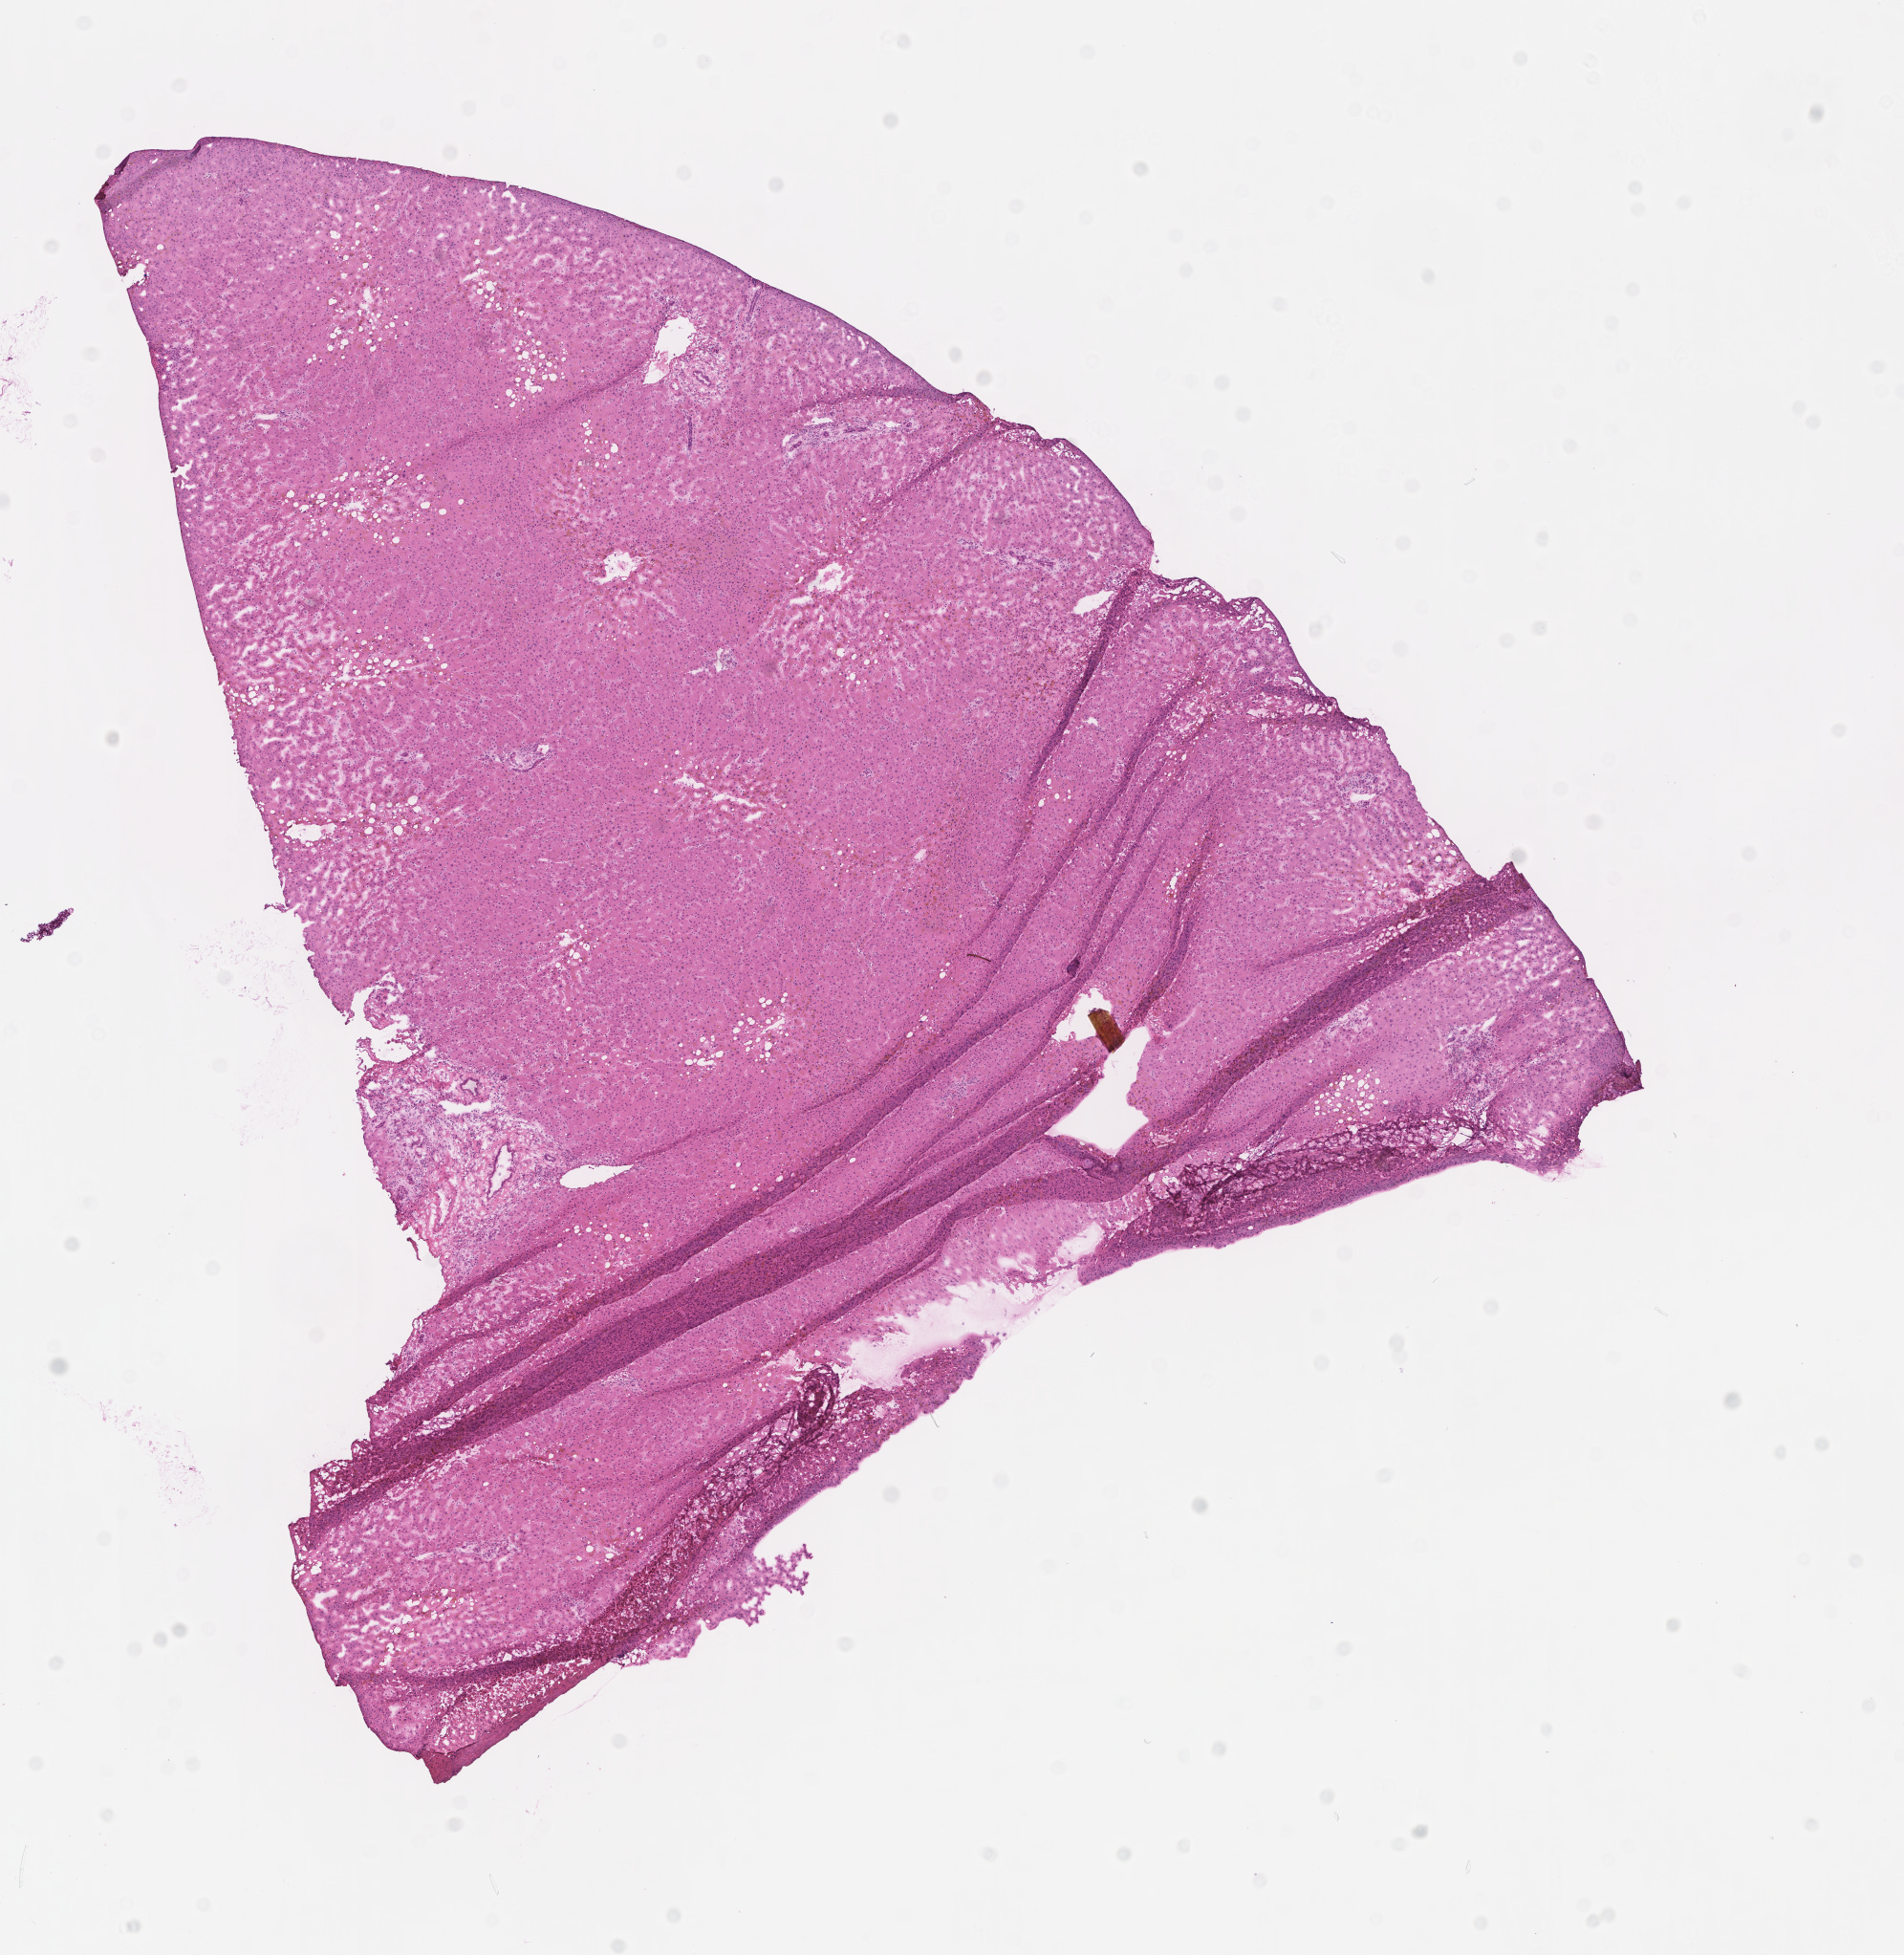
Digitized H&E-stained section — shown as a low-resolution overview of the whole scanned area (about 8.1 x 8.3 mm), frozen section, specimen: normal-tissue sample (non-tumor) from a patient with adenocarcinoma, NOS, site: colon. Male patient; age at initial diagnosis 61 years. Pathologist review of this section (percent, as recorded): tumor cells 2%, tumor nuclei 2%, stromal cells 0%, necrosis 0%, normal cells 98%. Infiltration values recorded for this section: lymphocyte infiltration 0%, monocyte infiltration 0%, neutrophil infiltration 0%.
- this section: non-tumor tissue sample; the patient's diagnosis is given above